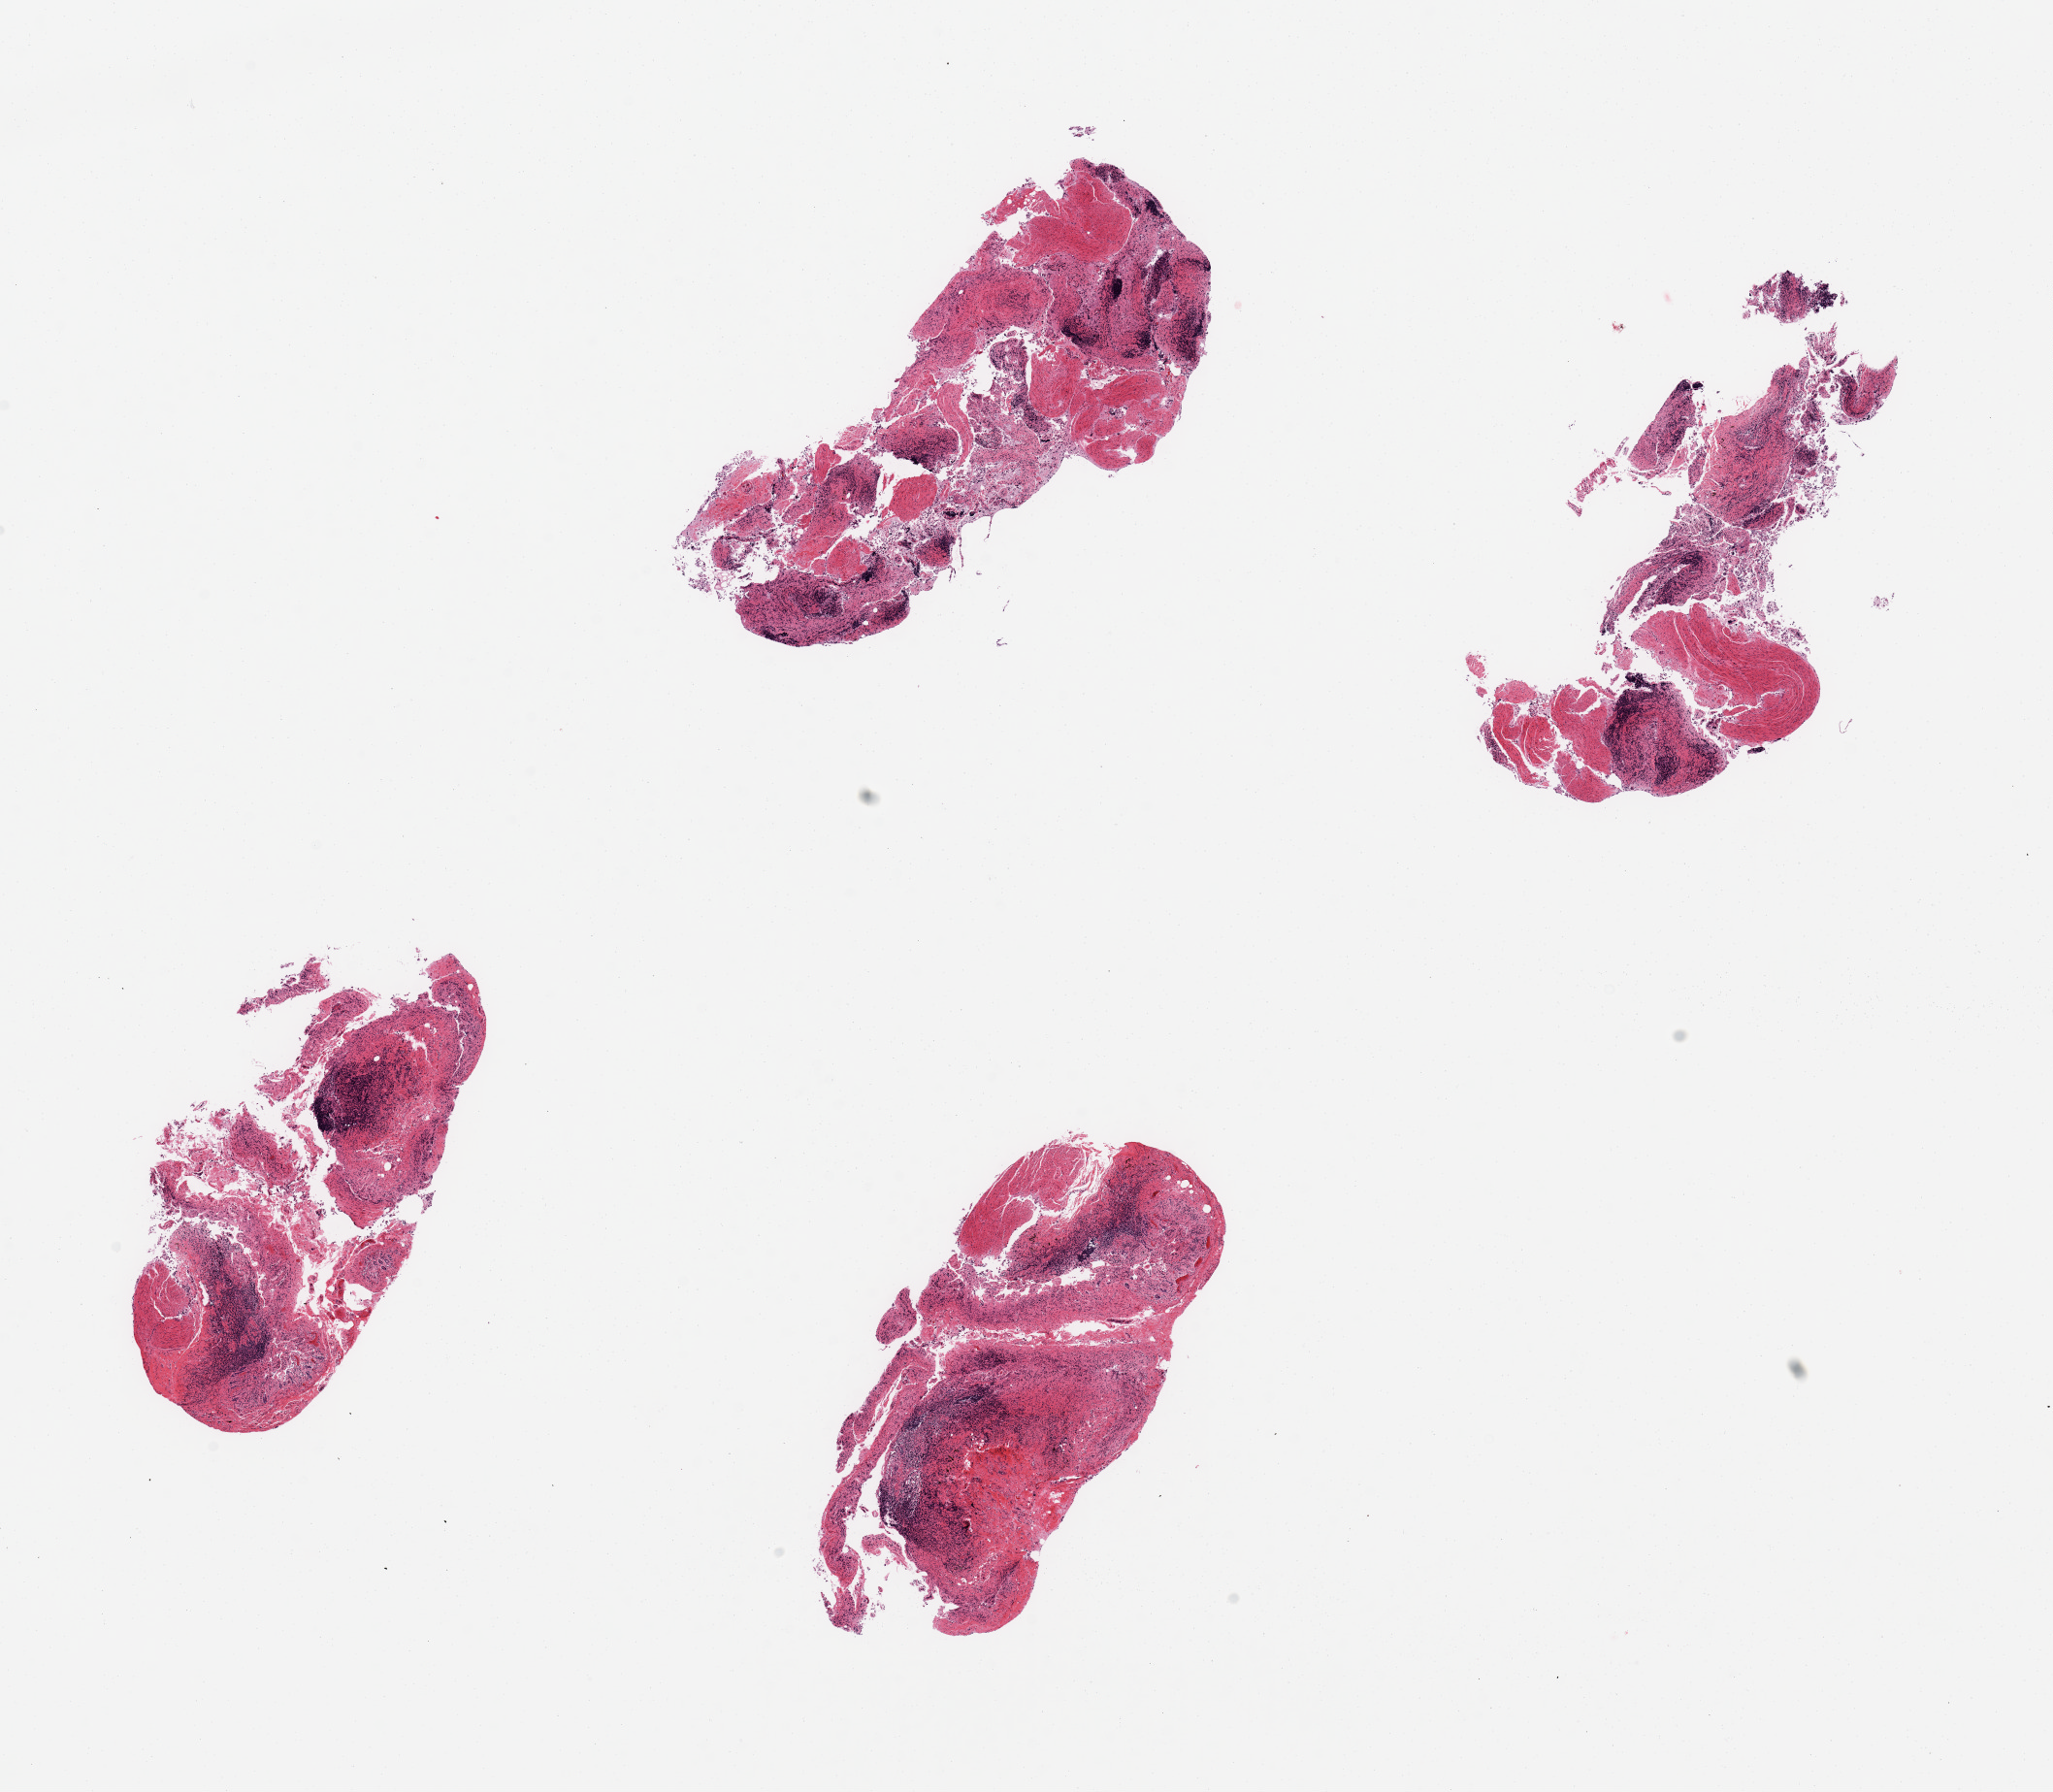
Hematoxylin and eosin (H&E) whole-slide image, brightfield, a low-resolution overview of the entire scanned area, about 16.7 x 14.6 mm; PAXgene-fixed, paraffin-embedded tissue; section of ileum (target tissue); donor tissue sample.
• pathologist's review note for this sample: 4 pieces, mucosa markedly autolyzed; lymphoid aggregates~20% lympphoid aggregates